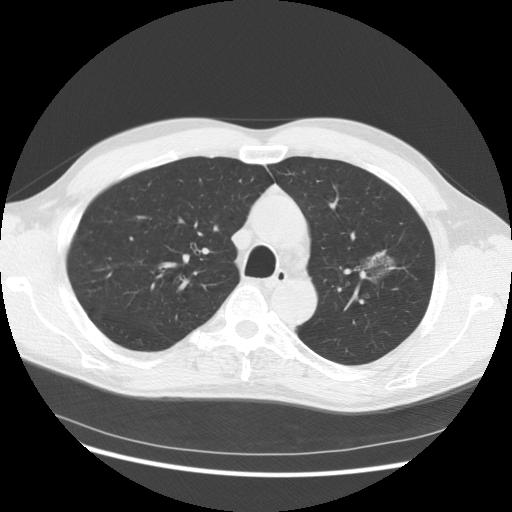
Chest CT (low-dose screening protocol), one axial image; third screening round (two years after baseline); lung window (W 1500 / L -600 HU); slice 99 of 145 in the series. Male participant, aged 61 years at enrolment. Former smoker at enrolment.
• Lesion marked by an expert reader, bounding box <333,225,415,306> (left, top, right, bottom; pixels).
• Screening reader's record for this exam (one nodule recorded; not confirmed to be the boxed lesion): non-calcified nodule or mass ≥4 mm, left upper lobe, 37 × 33 mm, poorly defined margins, mixed attenuation, pre-existing on the prior screen: yes; interval growth: yes.
• Official screen result: positive, other.
• Later outcome: lung cancer diagnosed 361 days after this screen — bronchiolo-alveolar adenocarcinoma, NOS, left upper lobe, well differentiated (G1), stage IB (AJCC 6th edition), 44 mm at pathology.